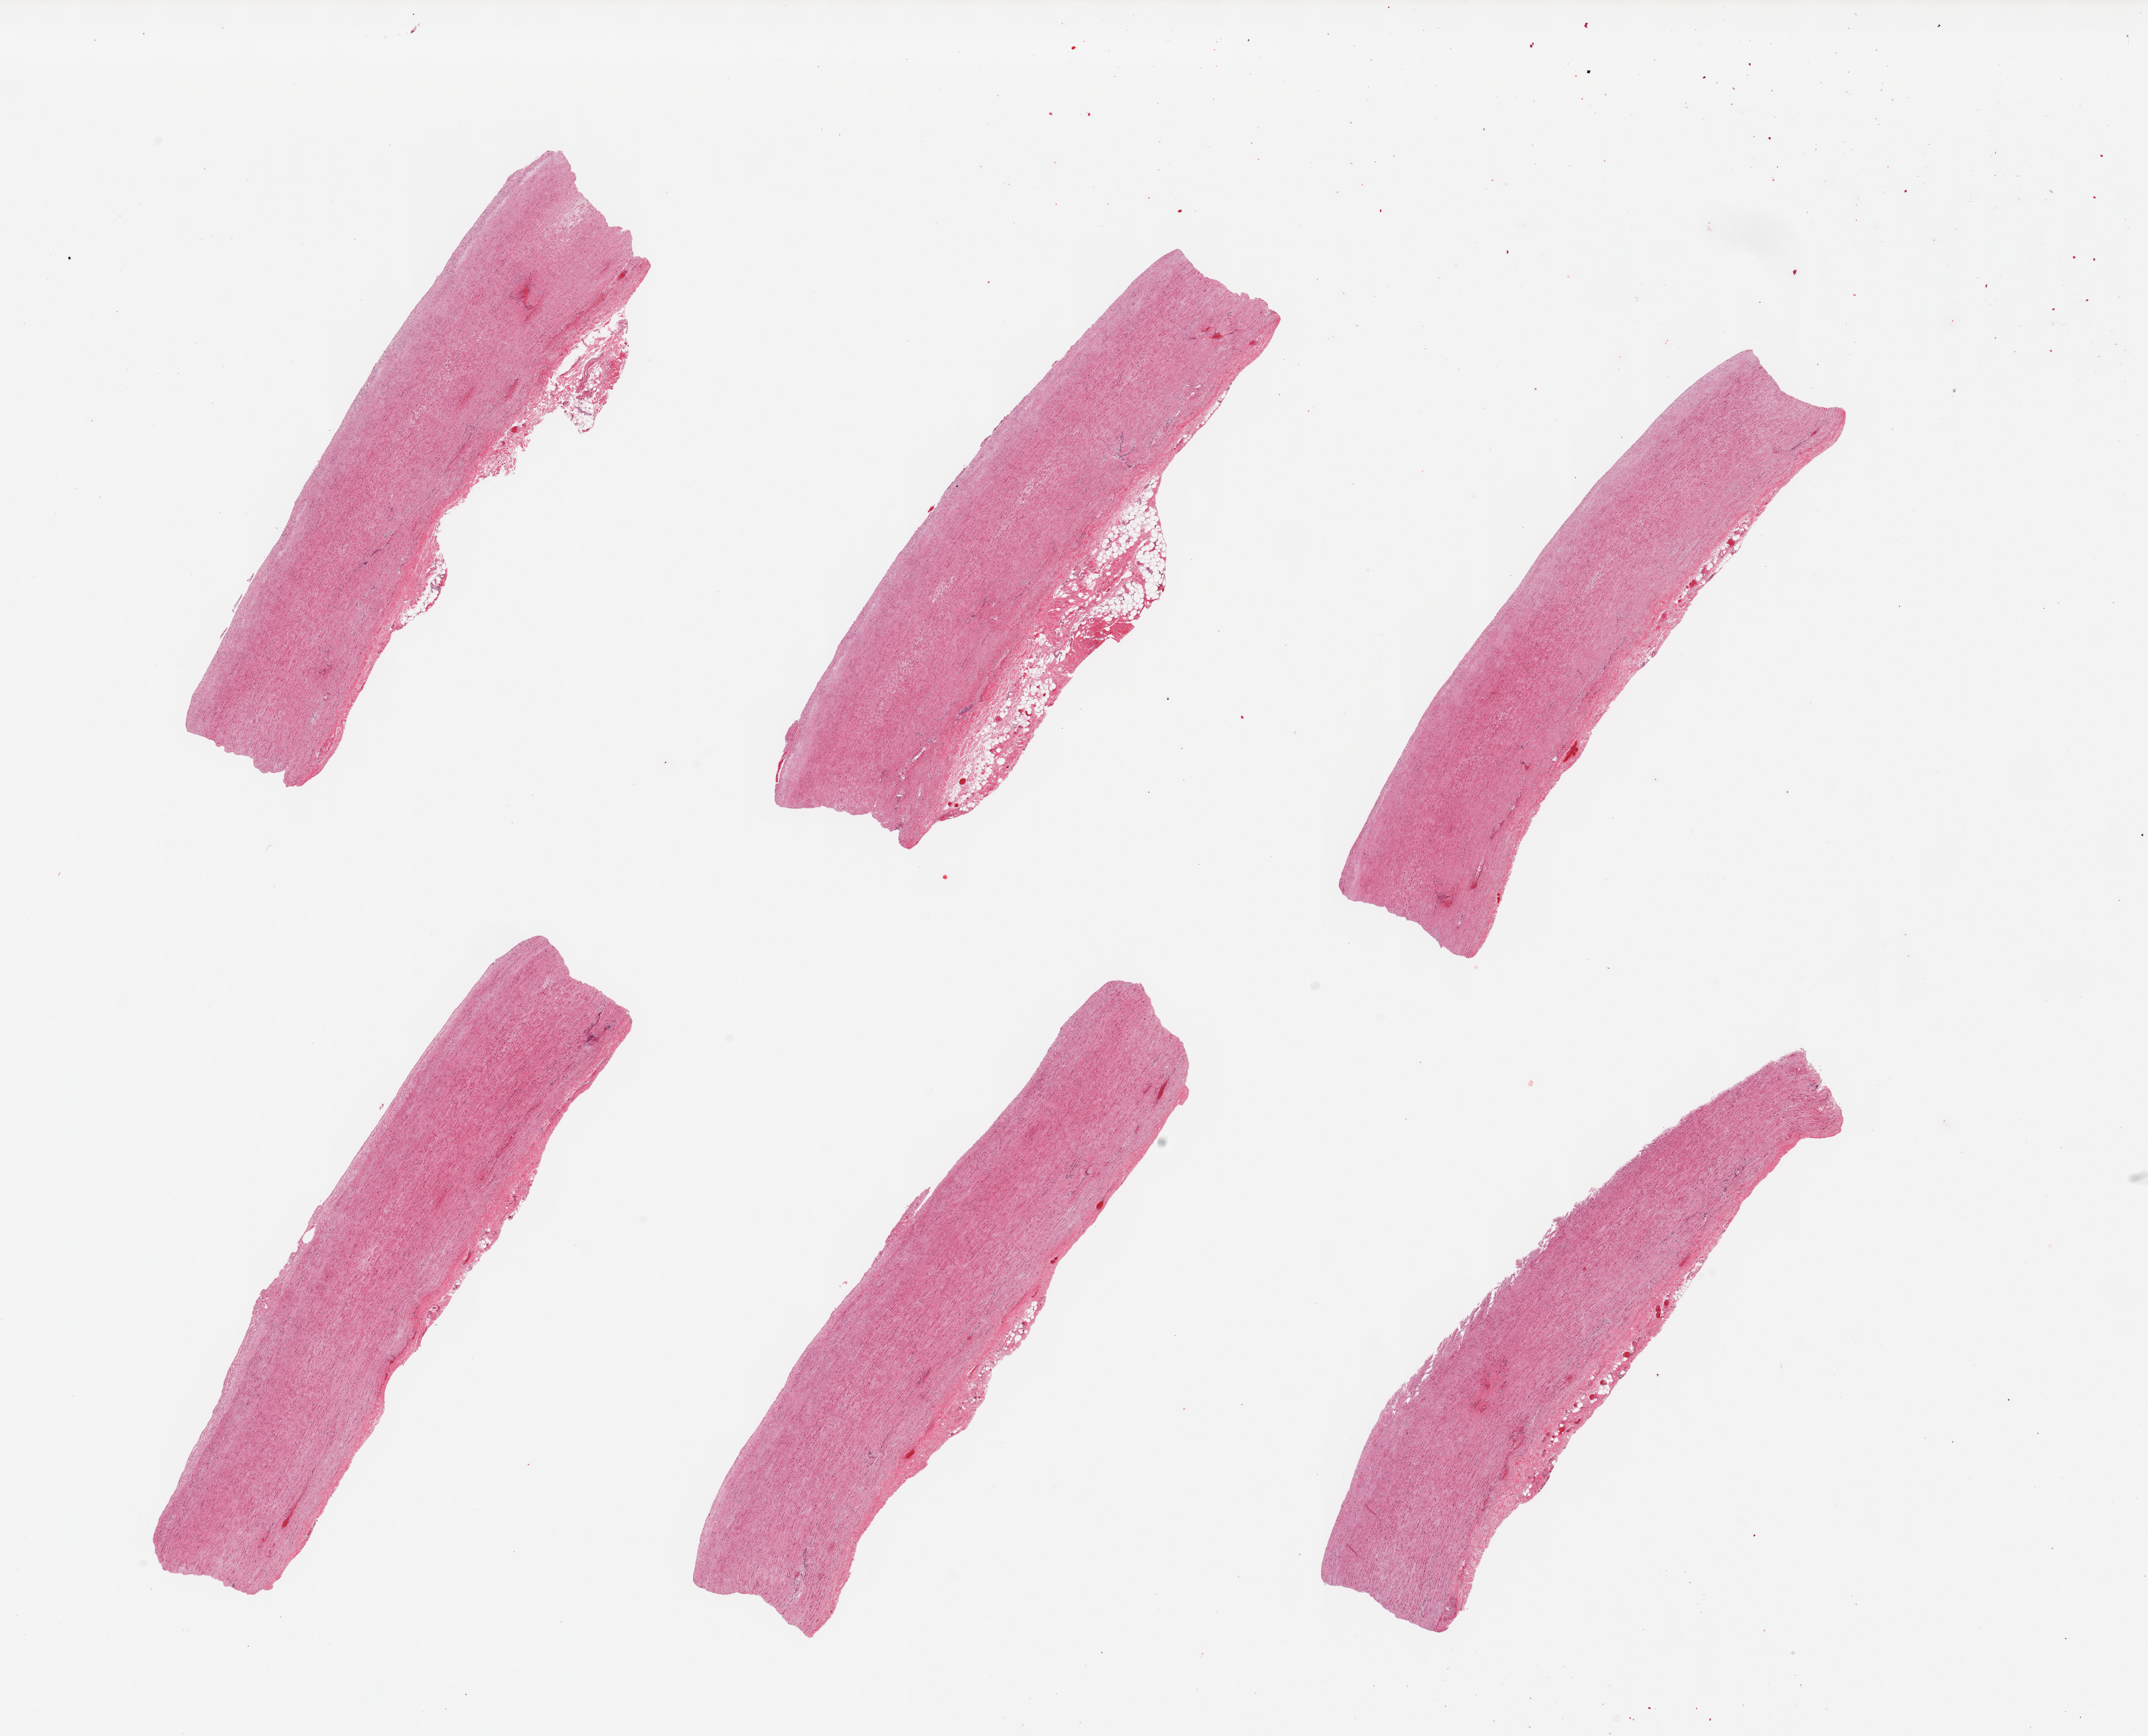
Whole-slide image, H&E stain — whole scanned area (about 25.6 x 20.7 mm) shown as a low-resolution overview; PAXgene-fixed, paraffin-embedded tissue; section of aorta (target tissue); tissue donor sample.
Review note (as recorded): 6 pieces; mild atherosclerosis.